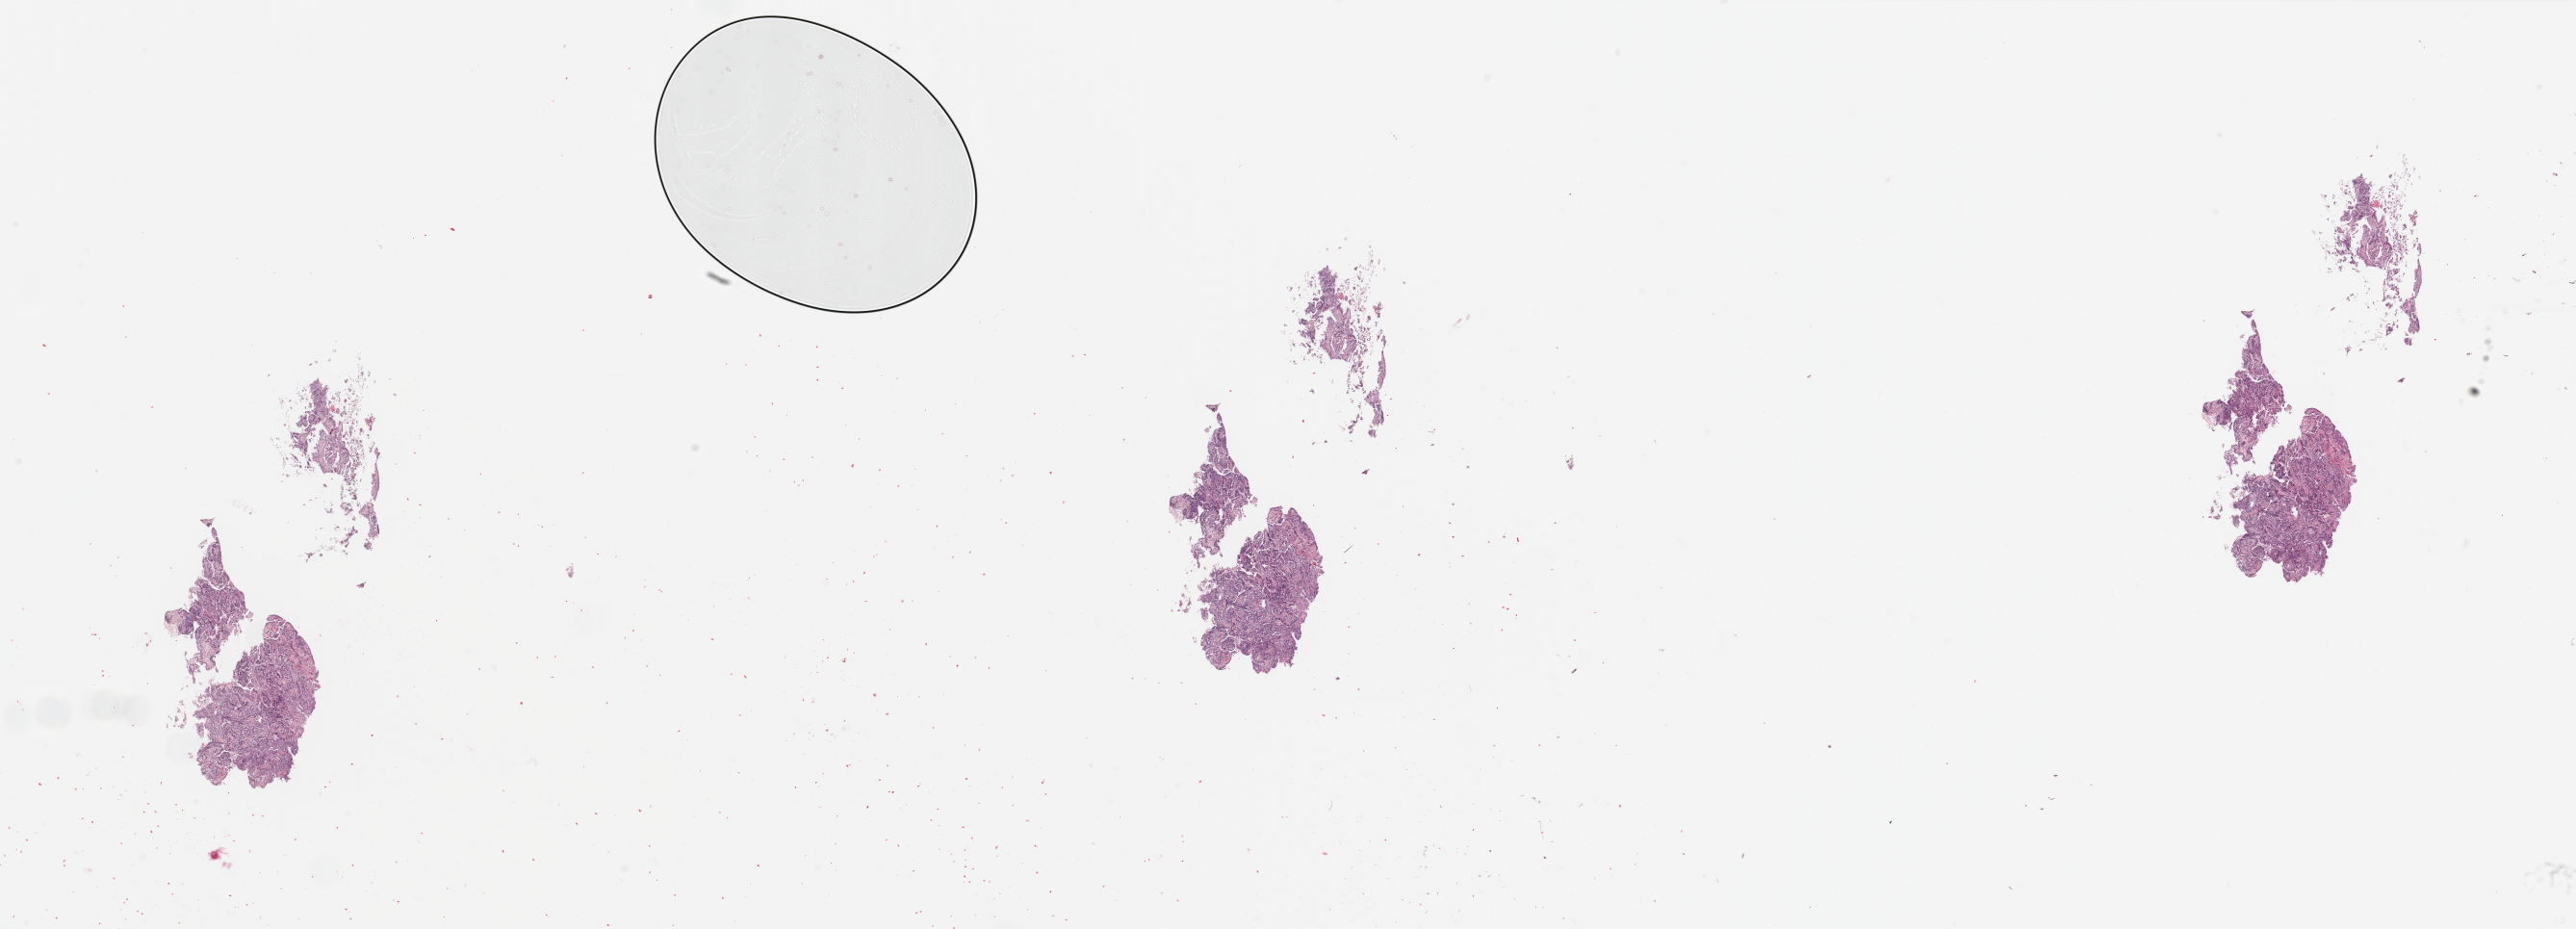
H&E whole-slide image, low-resolution overview of the scanned area, about 42.3 x 15.3 mm (acquisition: 20x scan); tumour tissue sample, sampled site: uterus. Female, 86 y/o. Histologic grade: G2 (moderately differentiated). Composition of this section per pathologist review: tumour nuclei 90%, necrosis 1%.
AJCC pathologic stage: IB. Diagnosis: Endometrioid adenocarcinoma, NOS.